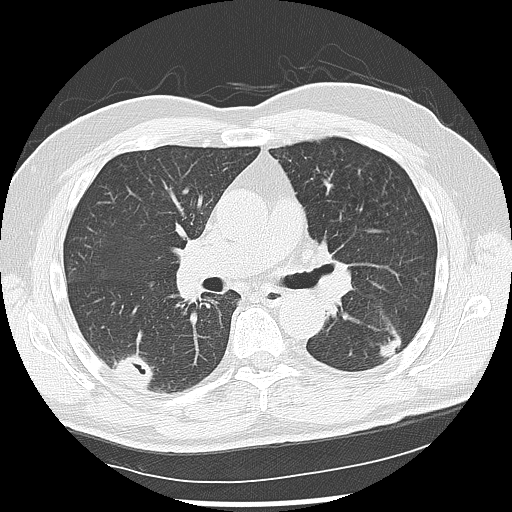
Low-dose screening chest CT, one axial slice; slice 75 of 142 in the series (ordered by position); reconstruction kernel LUNG; lung window (W 1500 / L -600 HU); 512 × 512 image matrix, field of view 360 × 360 mm.
Annotated regions visible in this slice (outlined manually by an expert reader):
- lesion 1 (nodule, lower lobe of left lung): bounding box <380,335,402,358> (left, top, right, bottom; pixels)
- lesion 2 (nodule, lower lobe of right lung): <113,355,154,388>